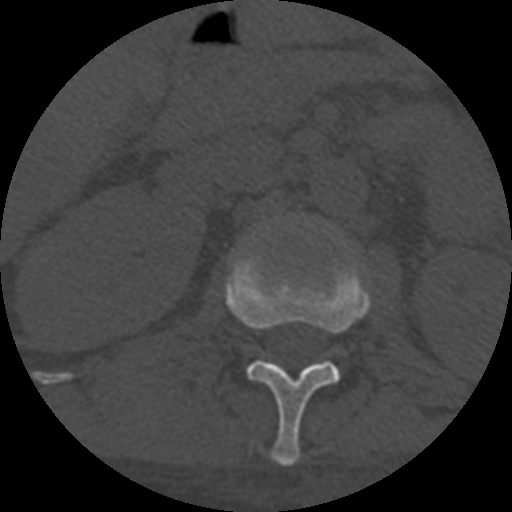
CT including the spine, one axial slice. Position 279 of 708 along the scan axis. Reconstruction kernel STANDARD. 120 kVp. One of 3 acquisitions stored at this slice position. Bone window (W 1800 / L 400 HU). 1.25 mm slice thickness. 512 × 512 image matrix. Patient age 55 years. From the clinical record (not read from this slice): primary cancer: colon; vertebrae with lytic lesions (as recorded): T12, L1, L5.
Structures marked on this image (semi-automatic segmentation, software-assisted and operator-edited):
- L1 vertebra: bounding box (x1, y1, x2, y2) in pixels: (225, 250, 371, 466)